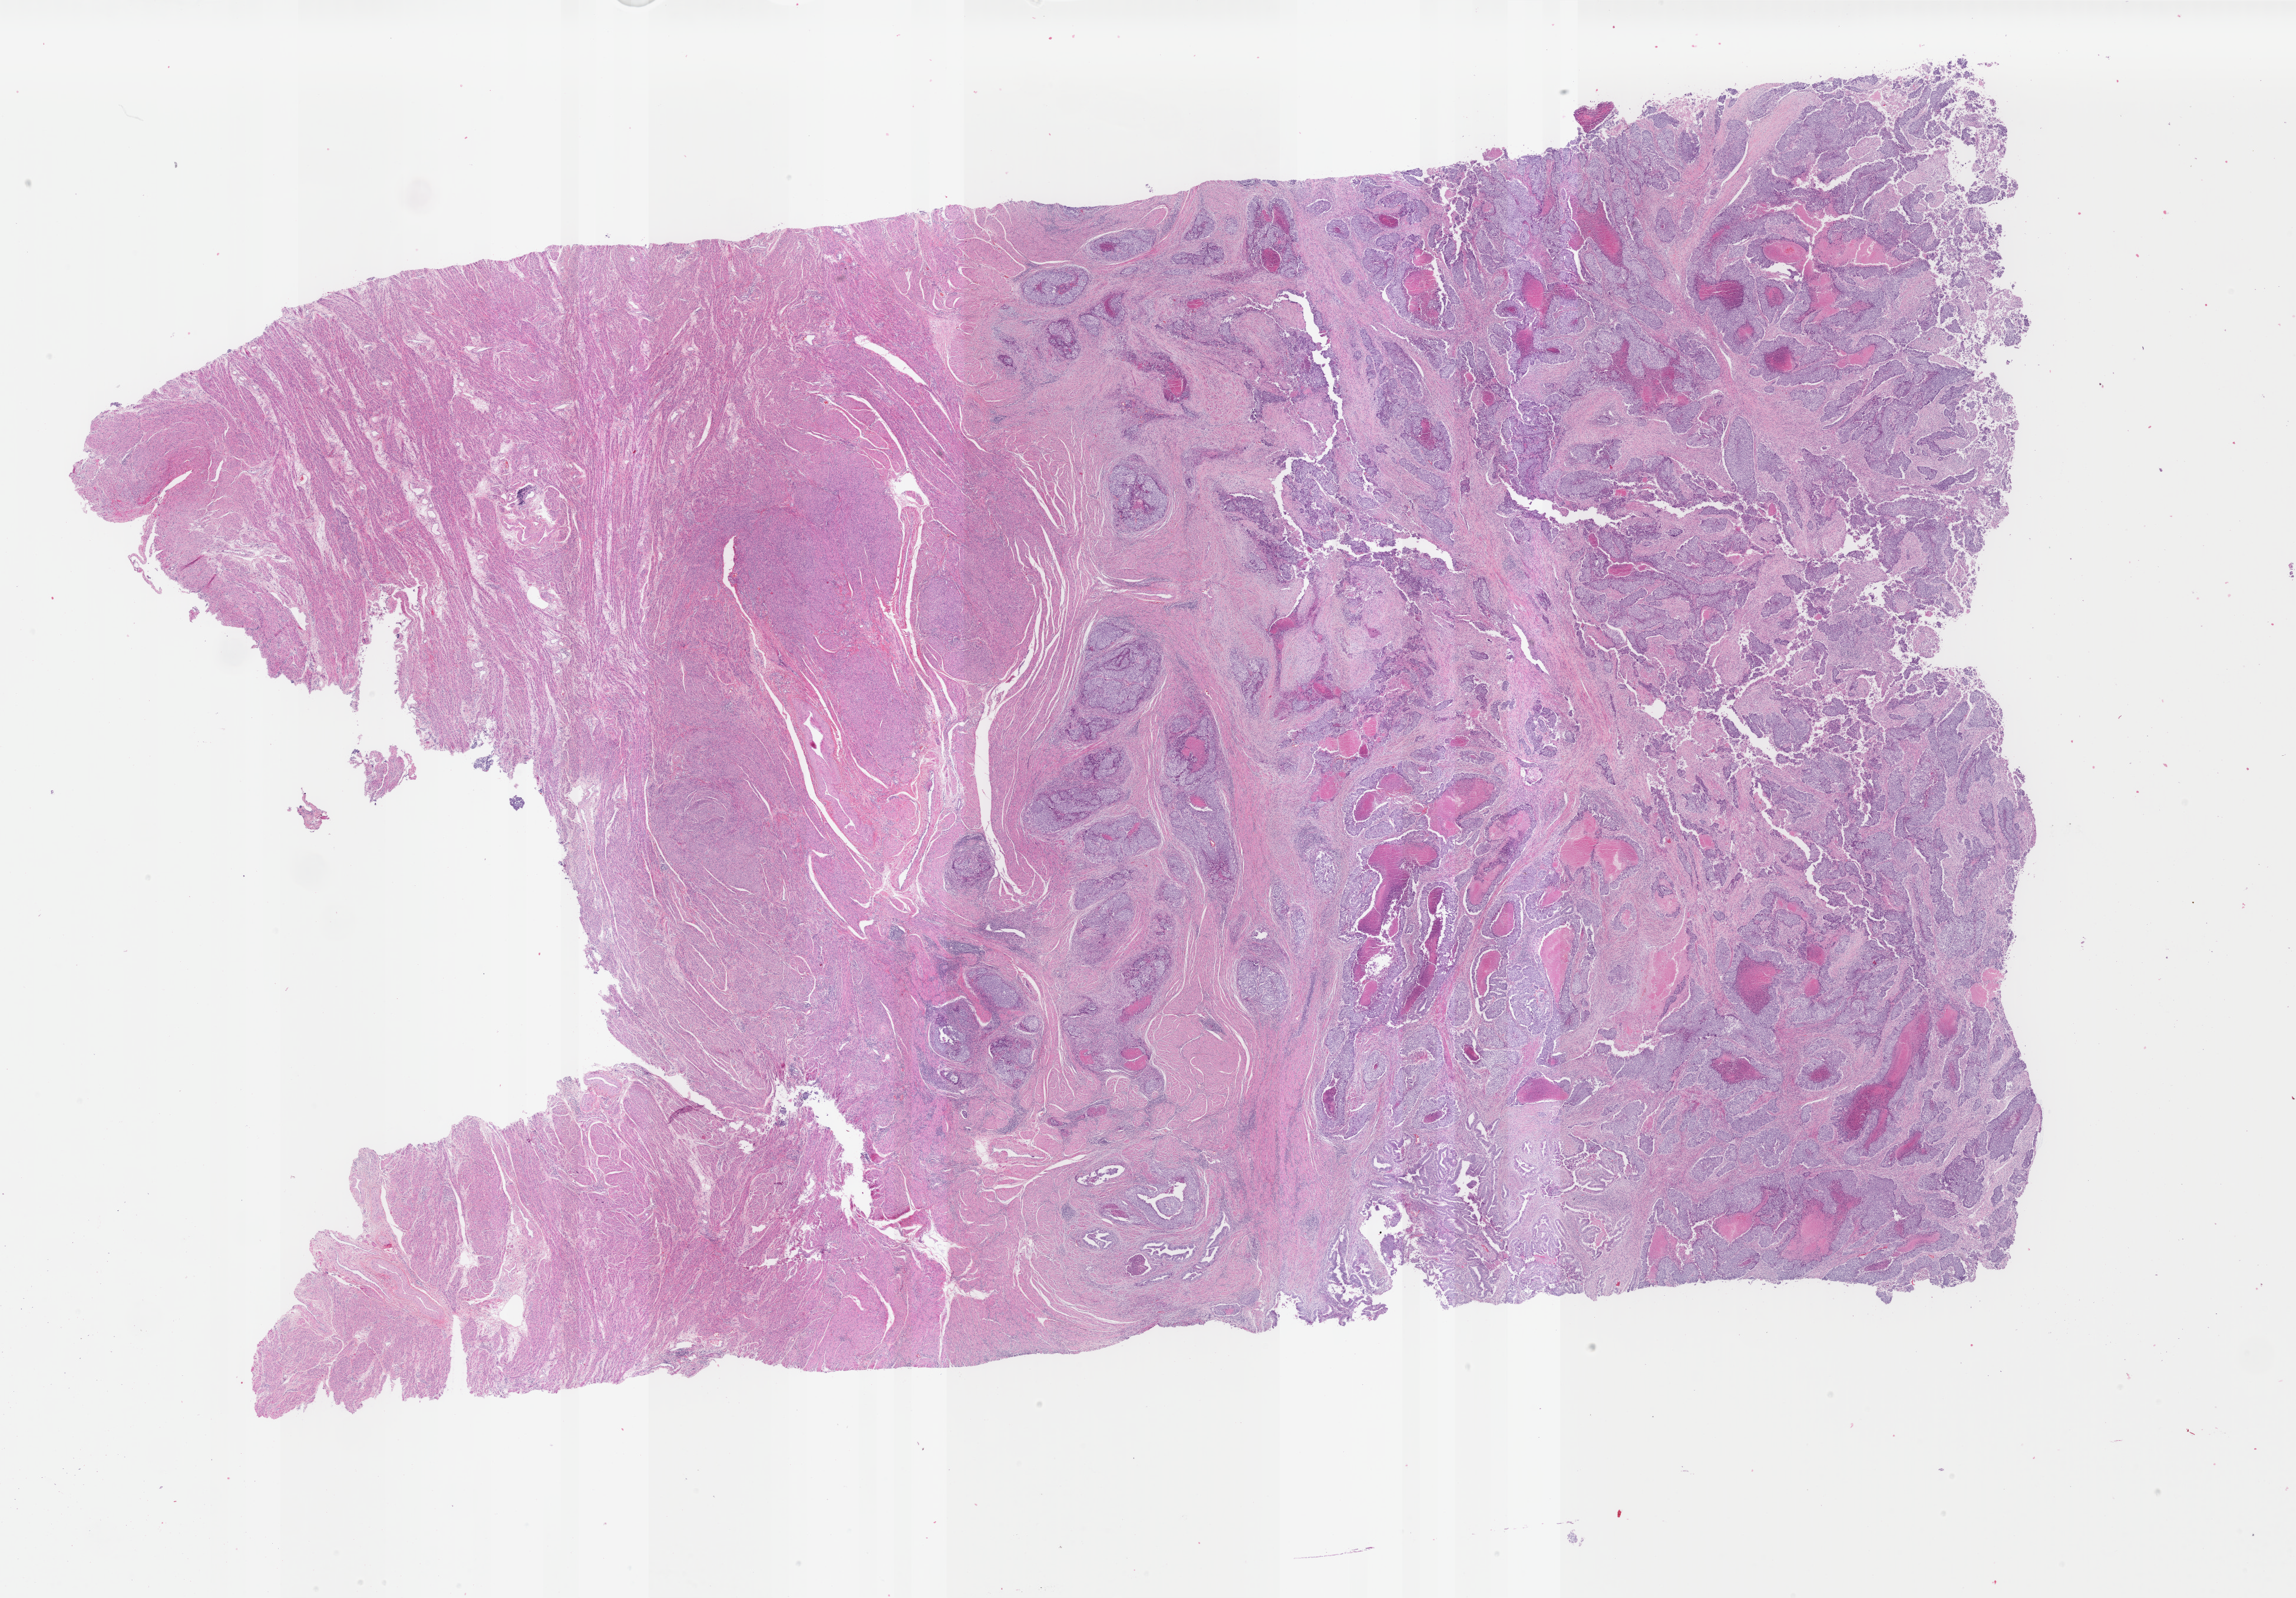
Digitized H&E tissue section (whole slide), shown as a low-resolution overview of the whole scanned area (about 30.9 x 21.5 mm). Formalin-fixed paraffin-embedded (FFPE) diagnostic section. Primary tumour sample from the uterus. Patient: female, age at initial diagnosis 53 years.
Pathologic diagnosis: Endometrioid adenocarcinoma, NOS (endometrium).